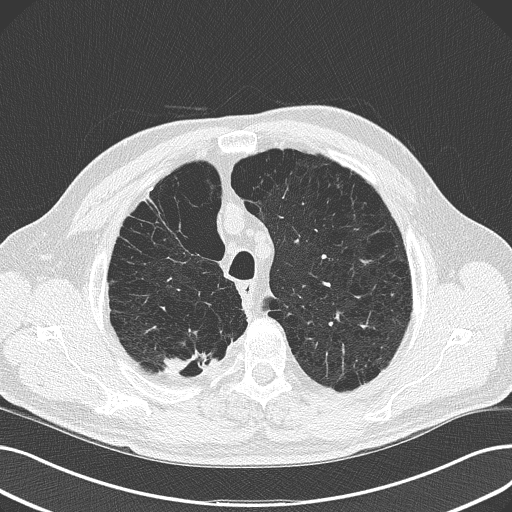
Low-dose screening chest CT, axial slice, second annual screen, lung window (W 1500 / L -600 HU), 2 mm slice thickness. Male participant, aged 68 years at enrolment. Current smoker at enrolment.
• Lesion marked by an expert reader, bounding box <143,333,226,393> (left, top, right, bottom; pixels).
• The screening reader recorded 4 non-calcified nodules or masses ≥4 mm on this exam (right upper lobe, left lower lobe, left upper lobe, right lower lobe); which of them this box marks is not recorded.
• Official screen result: positive, other.